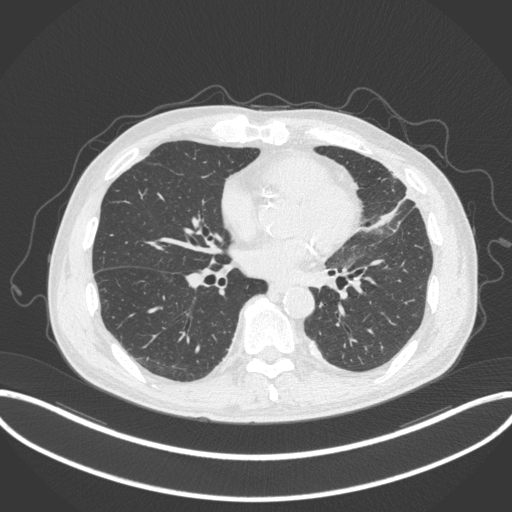
Chest CT, one axial slice. Position 143 of 382 along the scan axis. Lung window (W 1500 / L -600 HU). 1 mm slice thickness. 512 × 512 image matrix, field of view 415 × 415 mm. Male patient, age 64 years. From the clinical record (not read from this slice): clinical TNM (as recorded): T4 N1 M0; histopathological grade: G3.
Annotated regions visible in this slice (bounding box drawn by a radiologist):
- lung tumour (recorded histology: adenocarcinoma): bounding box <358,195,408,236> (left, top, right, bottom; pixels)